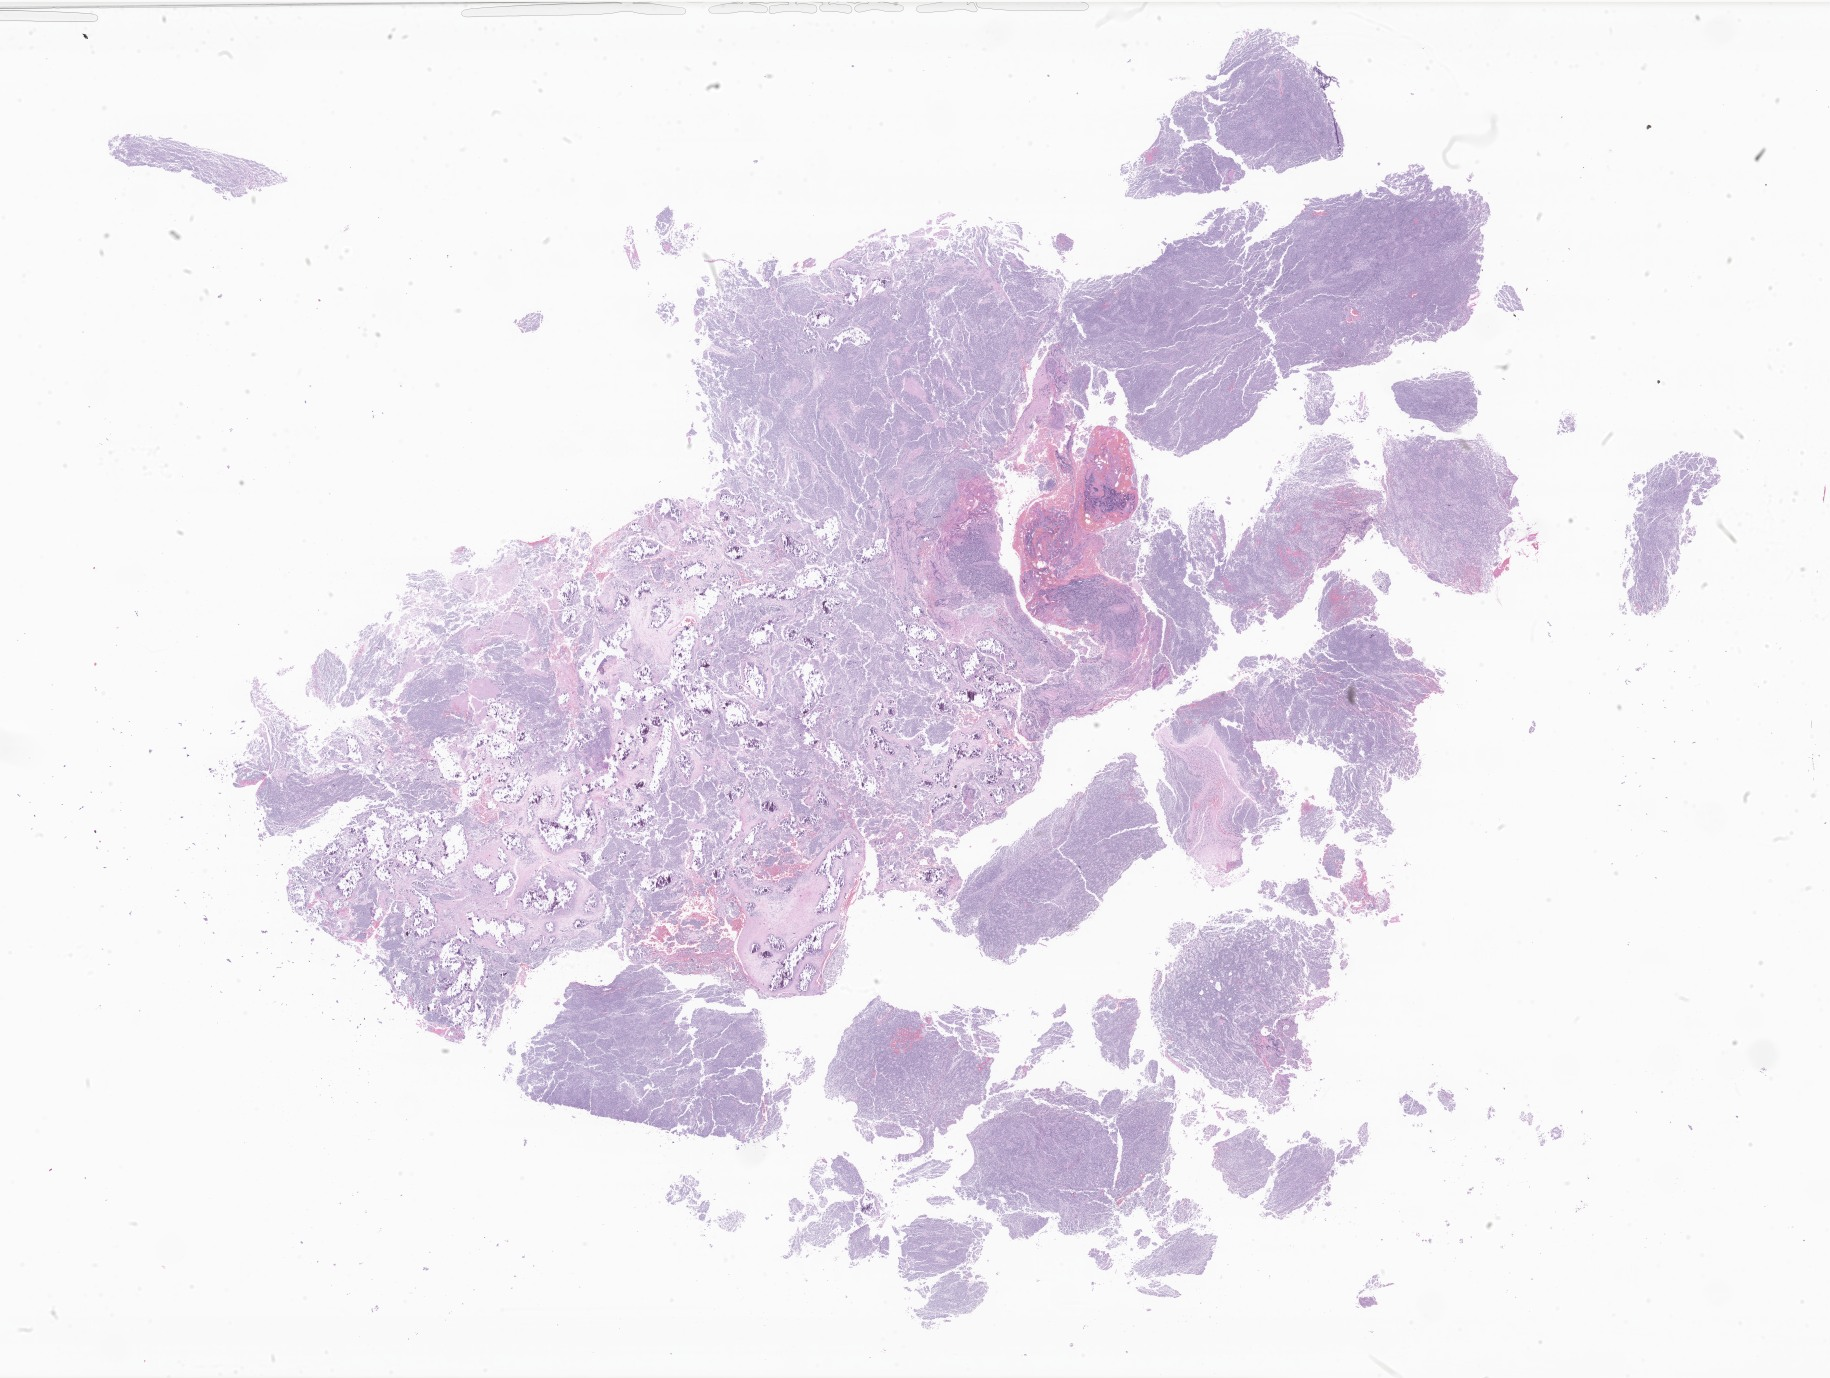
Digitized H&E-stained section of tumor tissue from the brain, whole scanned area (about 30.9 x 23.2 mm) shown as a low-resolution overview, formalin-fixed, paraffin-embedded (FFPE) tissue. Patient: female, age 163 months (13 years 7 months).
Diagnosis (ICD-O-3 morphology term): Medulloblastoma, NOS.